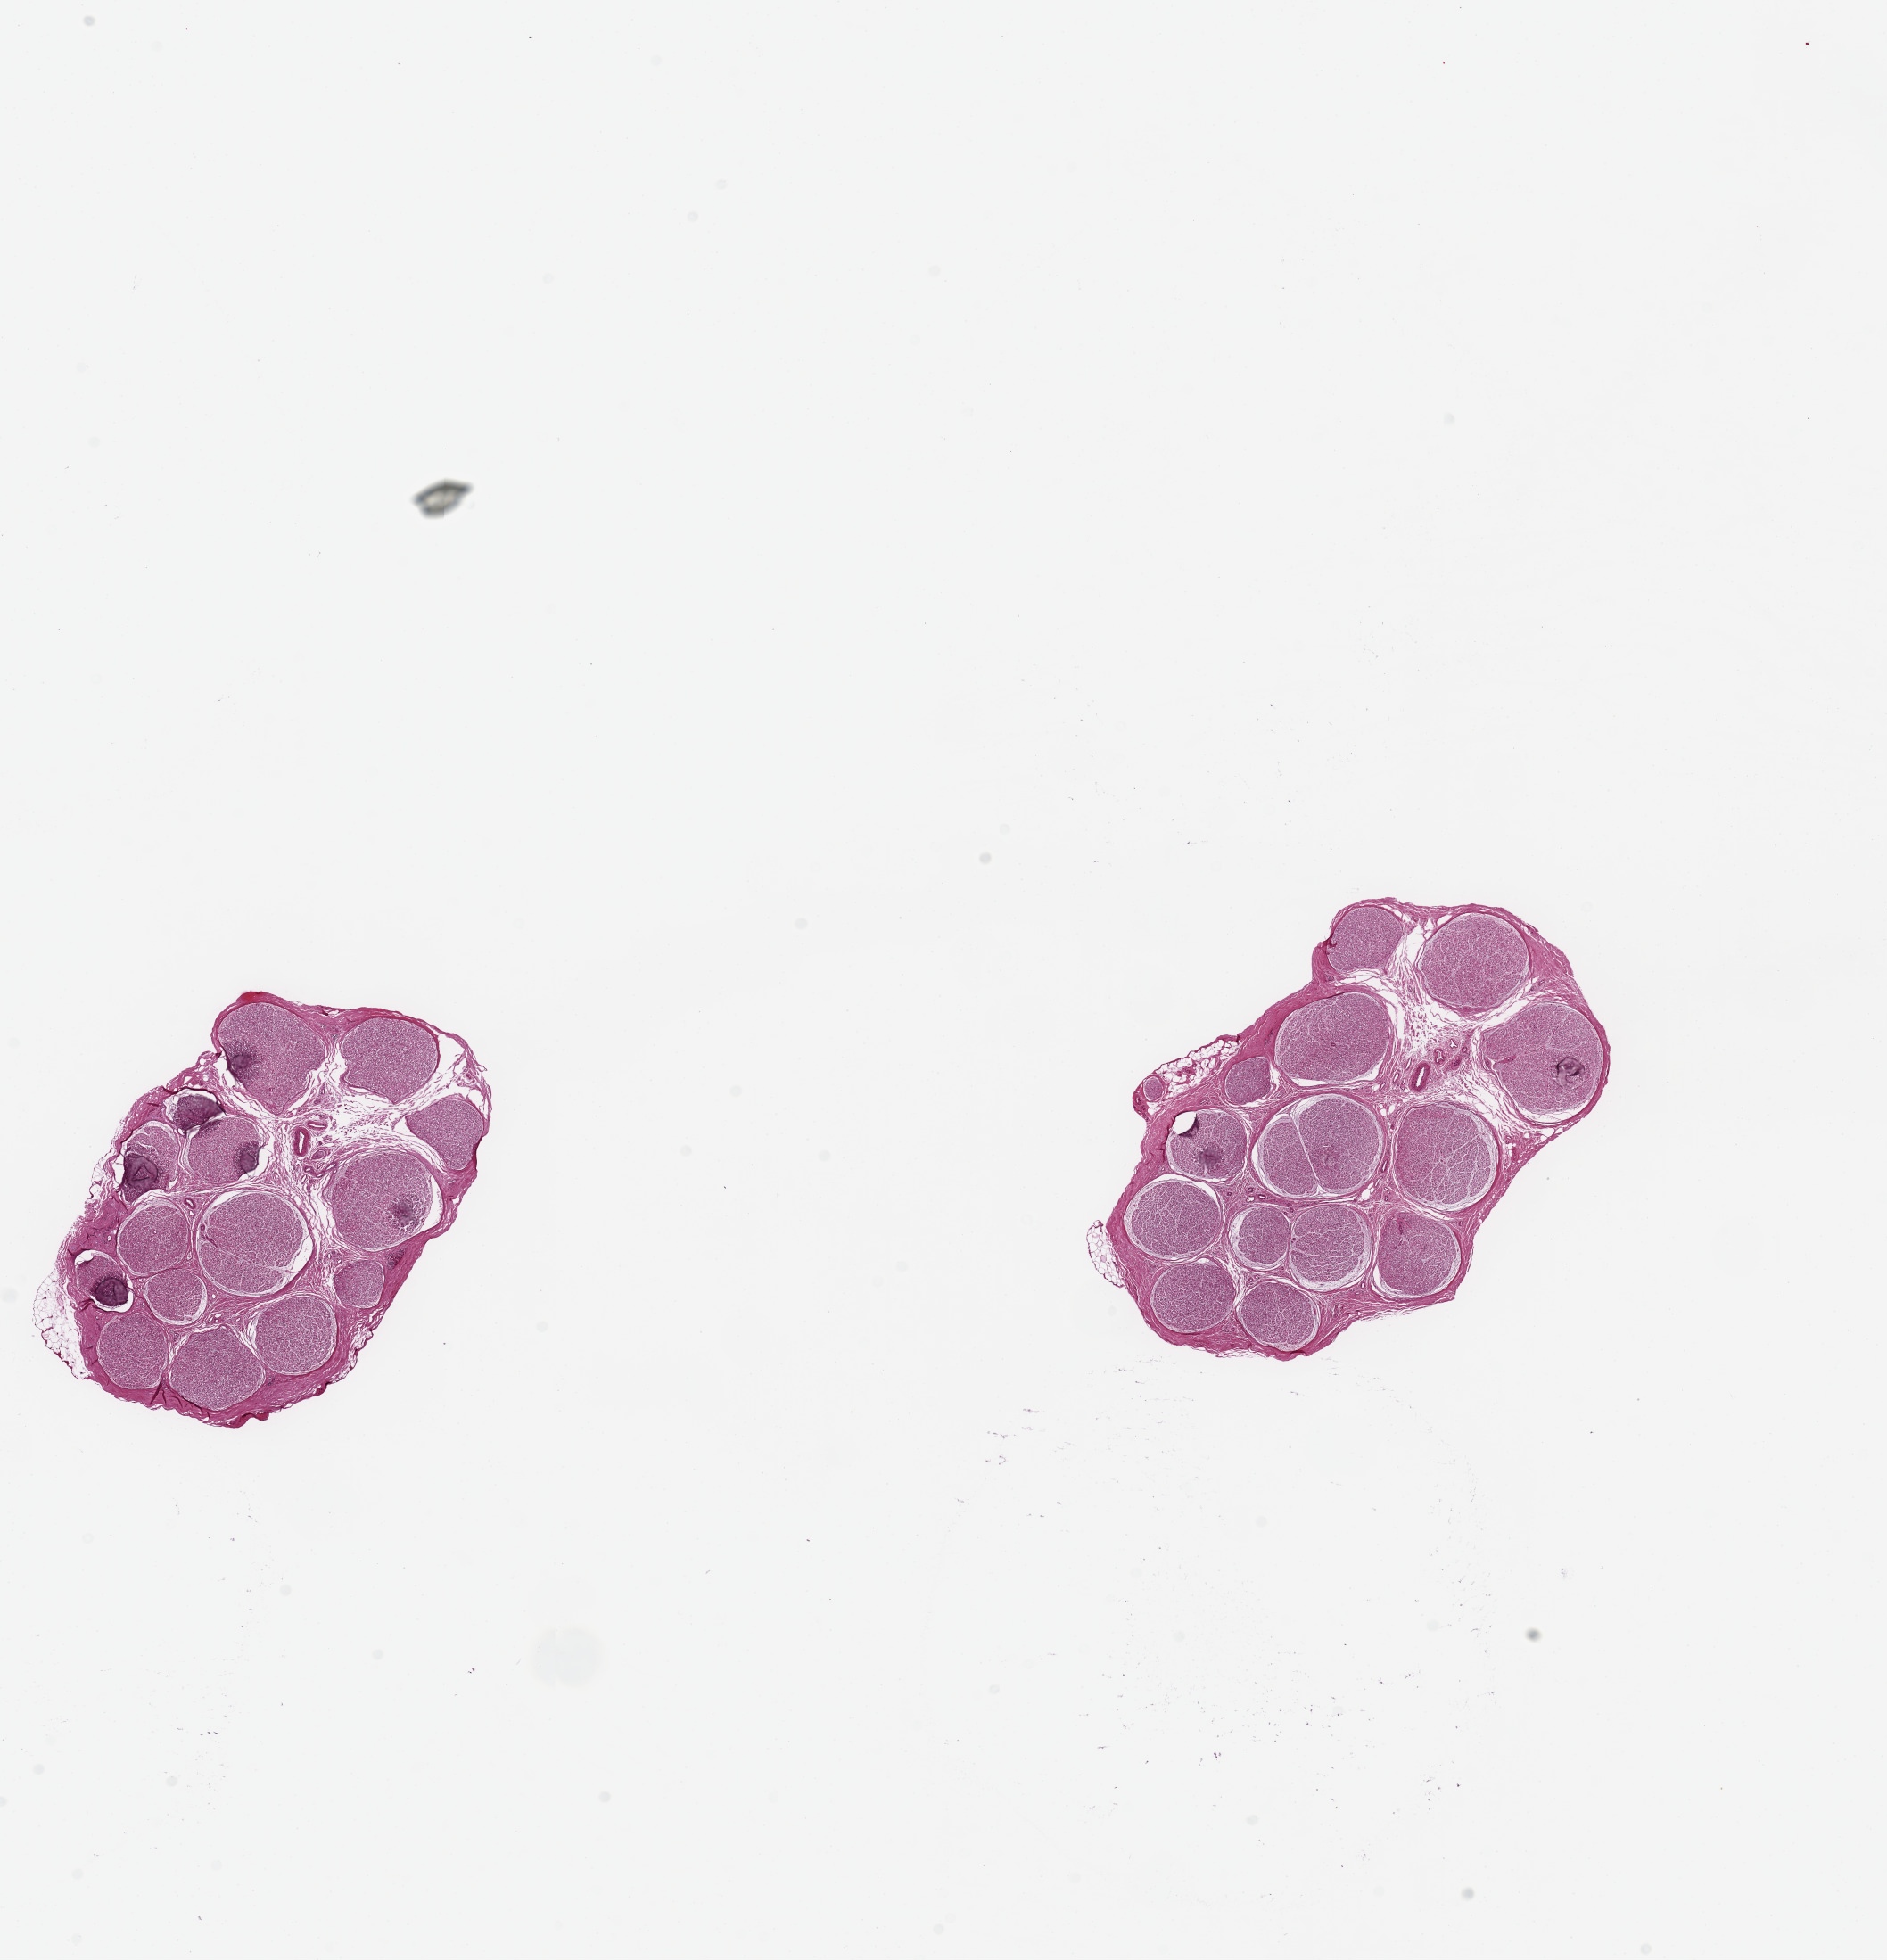
H&E whole-slide image, brightfield — shown as a low-resolution overview of the whole scanned area (about 16.7 x 17.4 mm); PAXgene-fixed paraffin-embedded (PFPE) section; sampled site (target tissue): tibial nerve; tissue donor sample.
* pathologist's review note for this sample: 2 pieces, 4x3 & 5x3mm; minimal external adipose